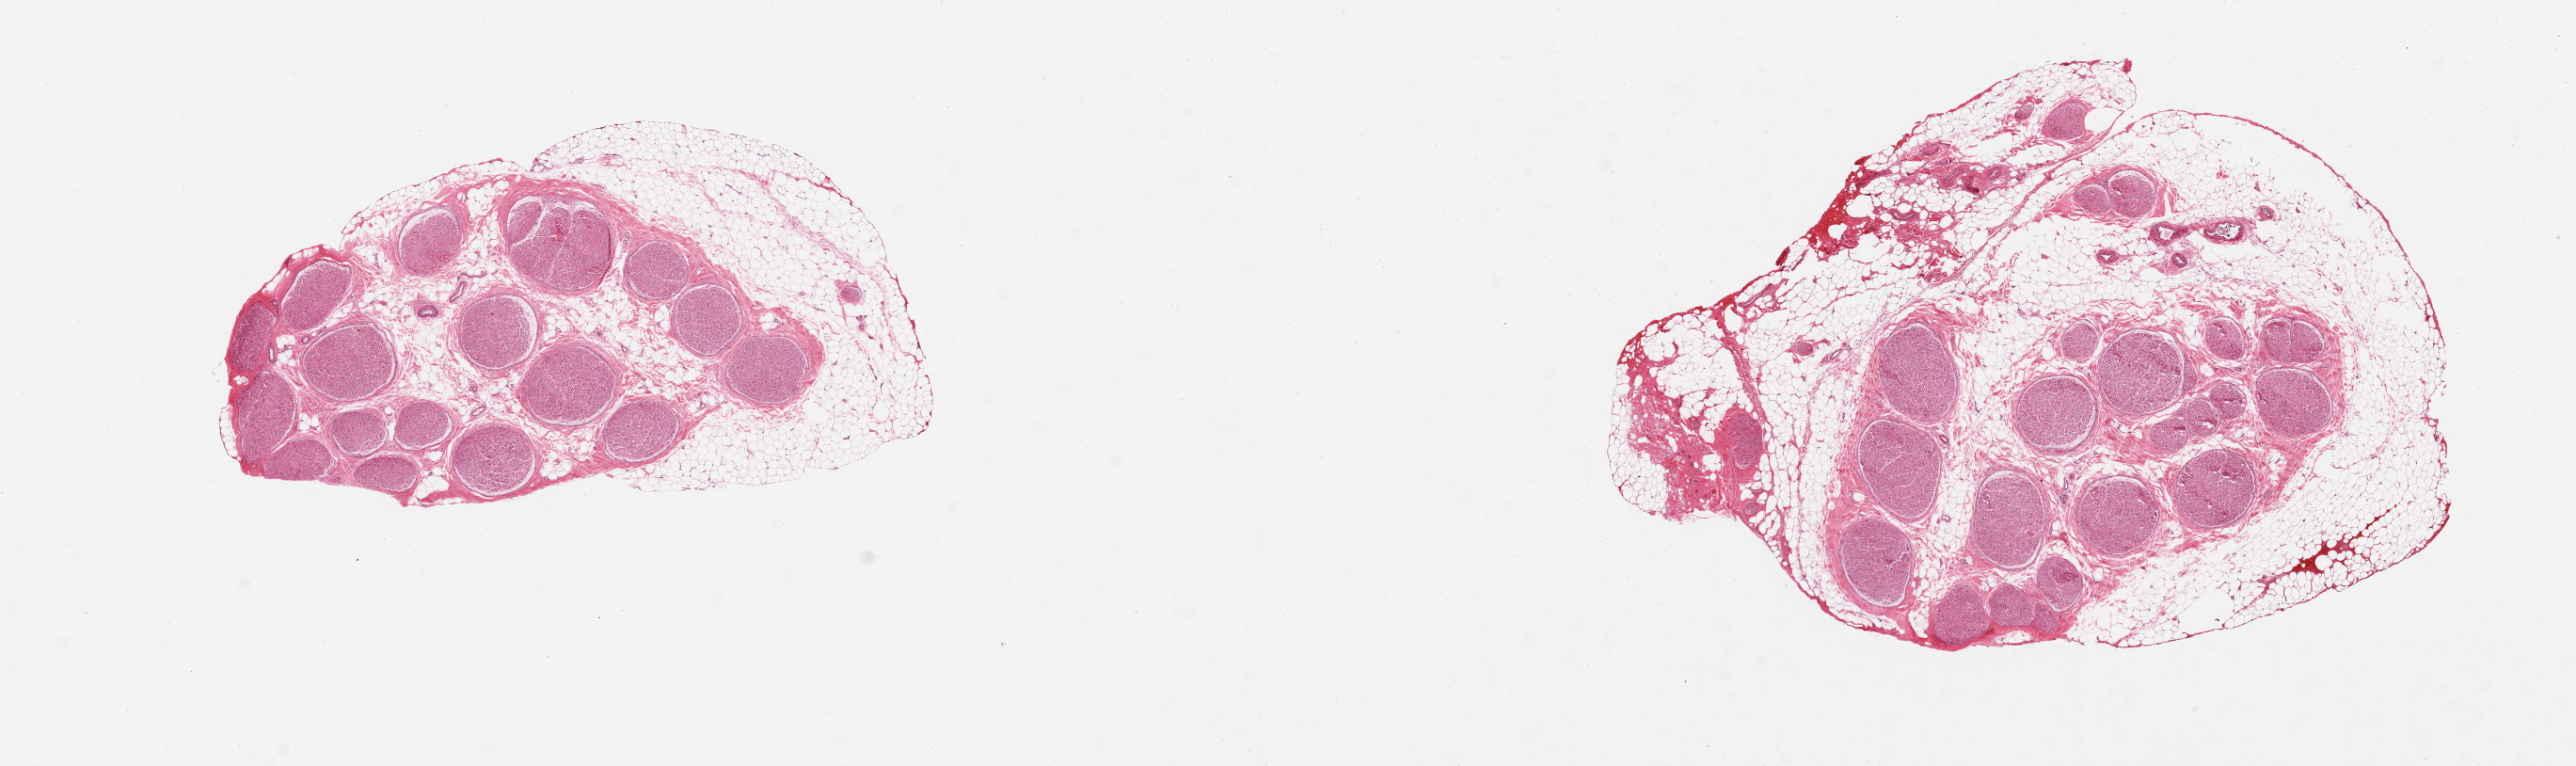
Whole-slide image, H&E stain — low-resolution overview of the scanned area, about 21.7 x 6.4 mm; PAXgene-fixed, paraffin-embedded tissue; section of tibial nerve (target tissue); donor tissue sample. Donor sex: female.
- reviewer comment on this tissue sample: 2 pieces, significant attached and internal adipose tissue on both pieces (30-60%)